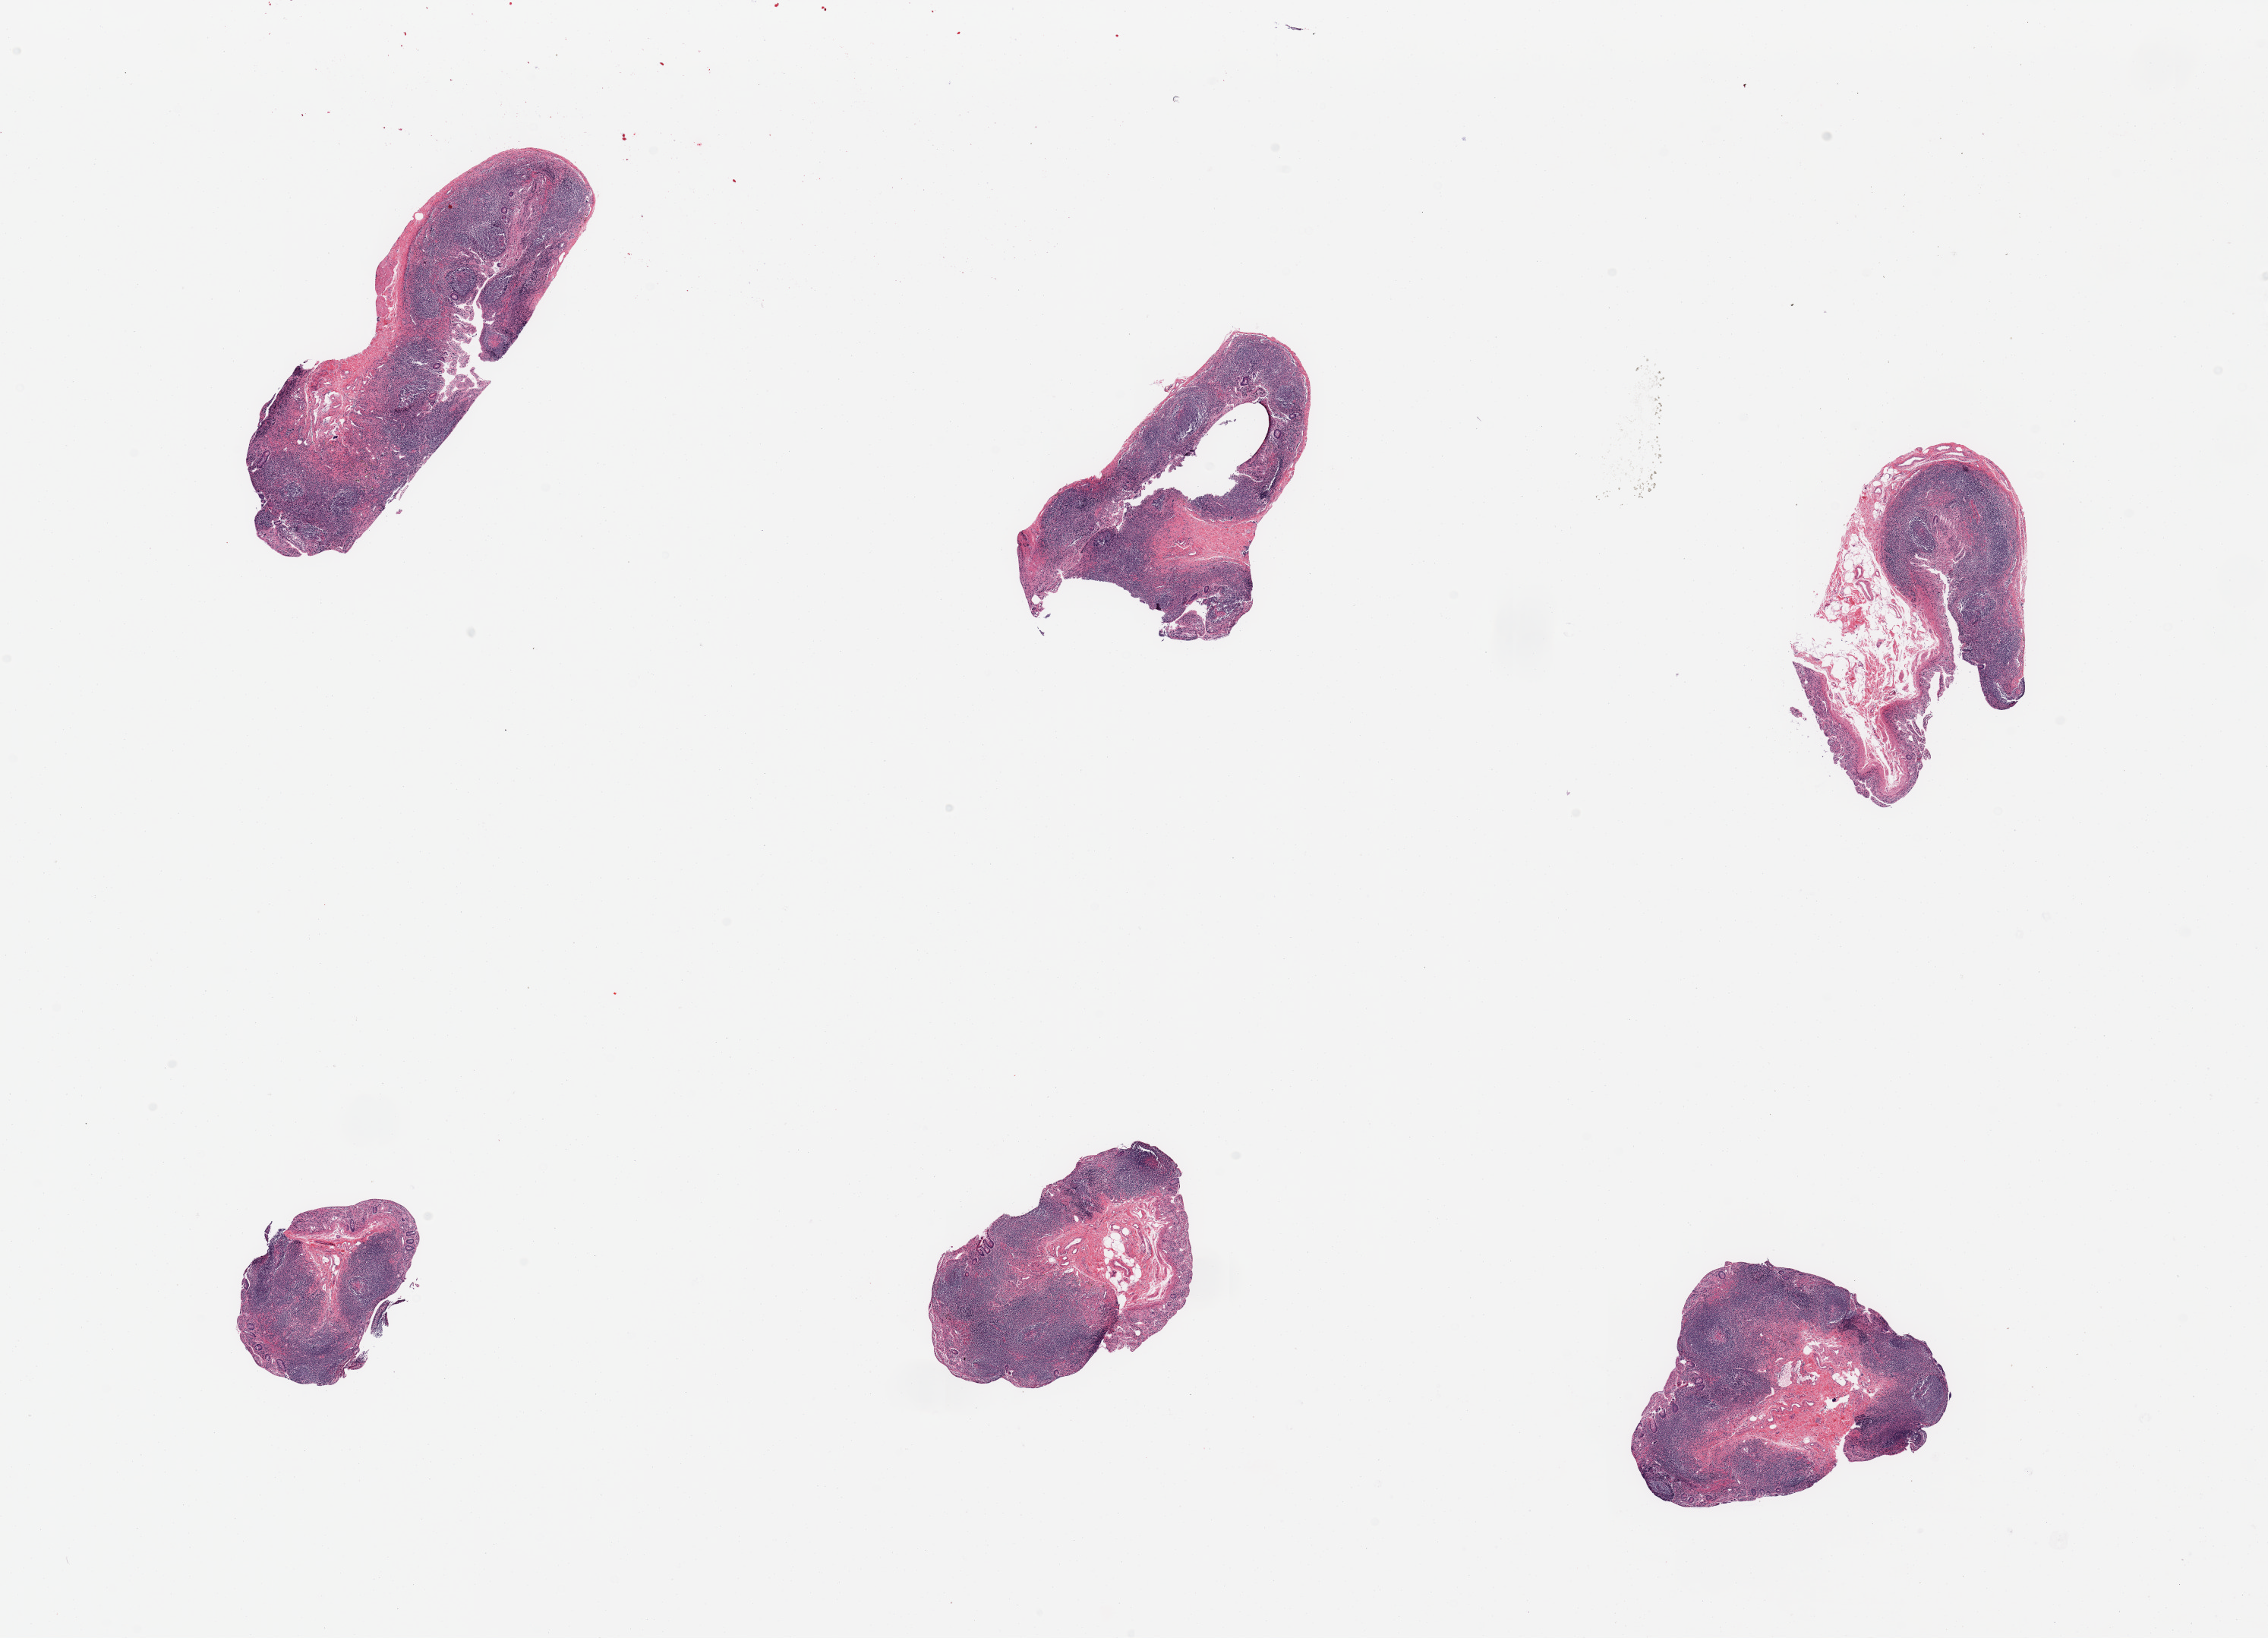
Digitized H&E-stained section, brightfield — whole scanned area (about 23.6 x 17.1 mm, acquisition: 20x scan) shown as a low-resolution overview, PAXgene-fixed paraffin-embedded (PFPE) section, sampled site (target tissue): ileum, donor tissue sample. Male donor.
Review note (as recorded): 6 pieces; all include abundant lymphoid tissue.